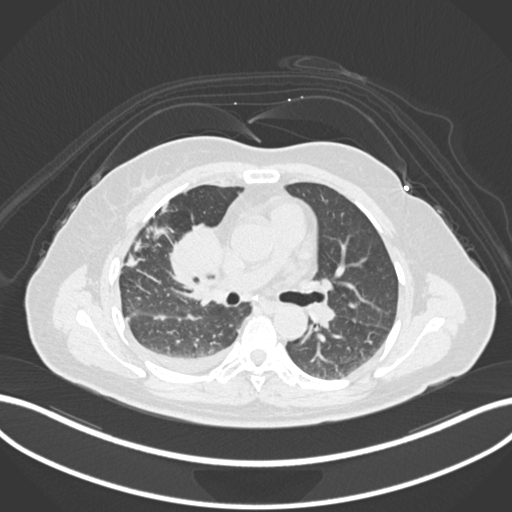
Chest CT, one axial slice. Slice 81 of 172 in the series (ordered by position). 120 kVp. Lung window (W 1500 / L -600 HU). 1 mm slice thickness. 512 × 512 image matrix, field of view 400 × 400 mm. Patient: female, 52 years. Case-level facts recorded for this patient, not image findings: clinical TNM (as recorded): T3 N1 M1.
Annotated regions visible in this slice (bounding box drawn by a radiologist):
- lung tumour (recorded histology: adenocarcinoma): bounding box <162,221,223,282> (left, top, right, bottom; pixels)